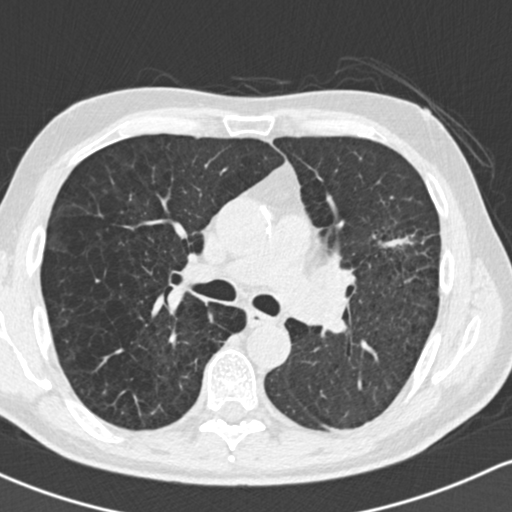
Low-dose screening chest CT, one axial slice. Position 93 of 162 along the scan axis. Reconstruction kernel B30f. Lung window (W 1500 / L -600 HU). 512 × 512 image matrix, field of view 318 × 318 mm.
Annotated regions visible in this slice (expert manual segmentation):
- lesion 1 (tumor, upper lobe of left lung): bounding box [x1, y1, x2, y2] px = [379, 235, 413, 248]